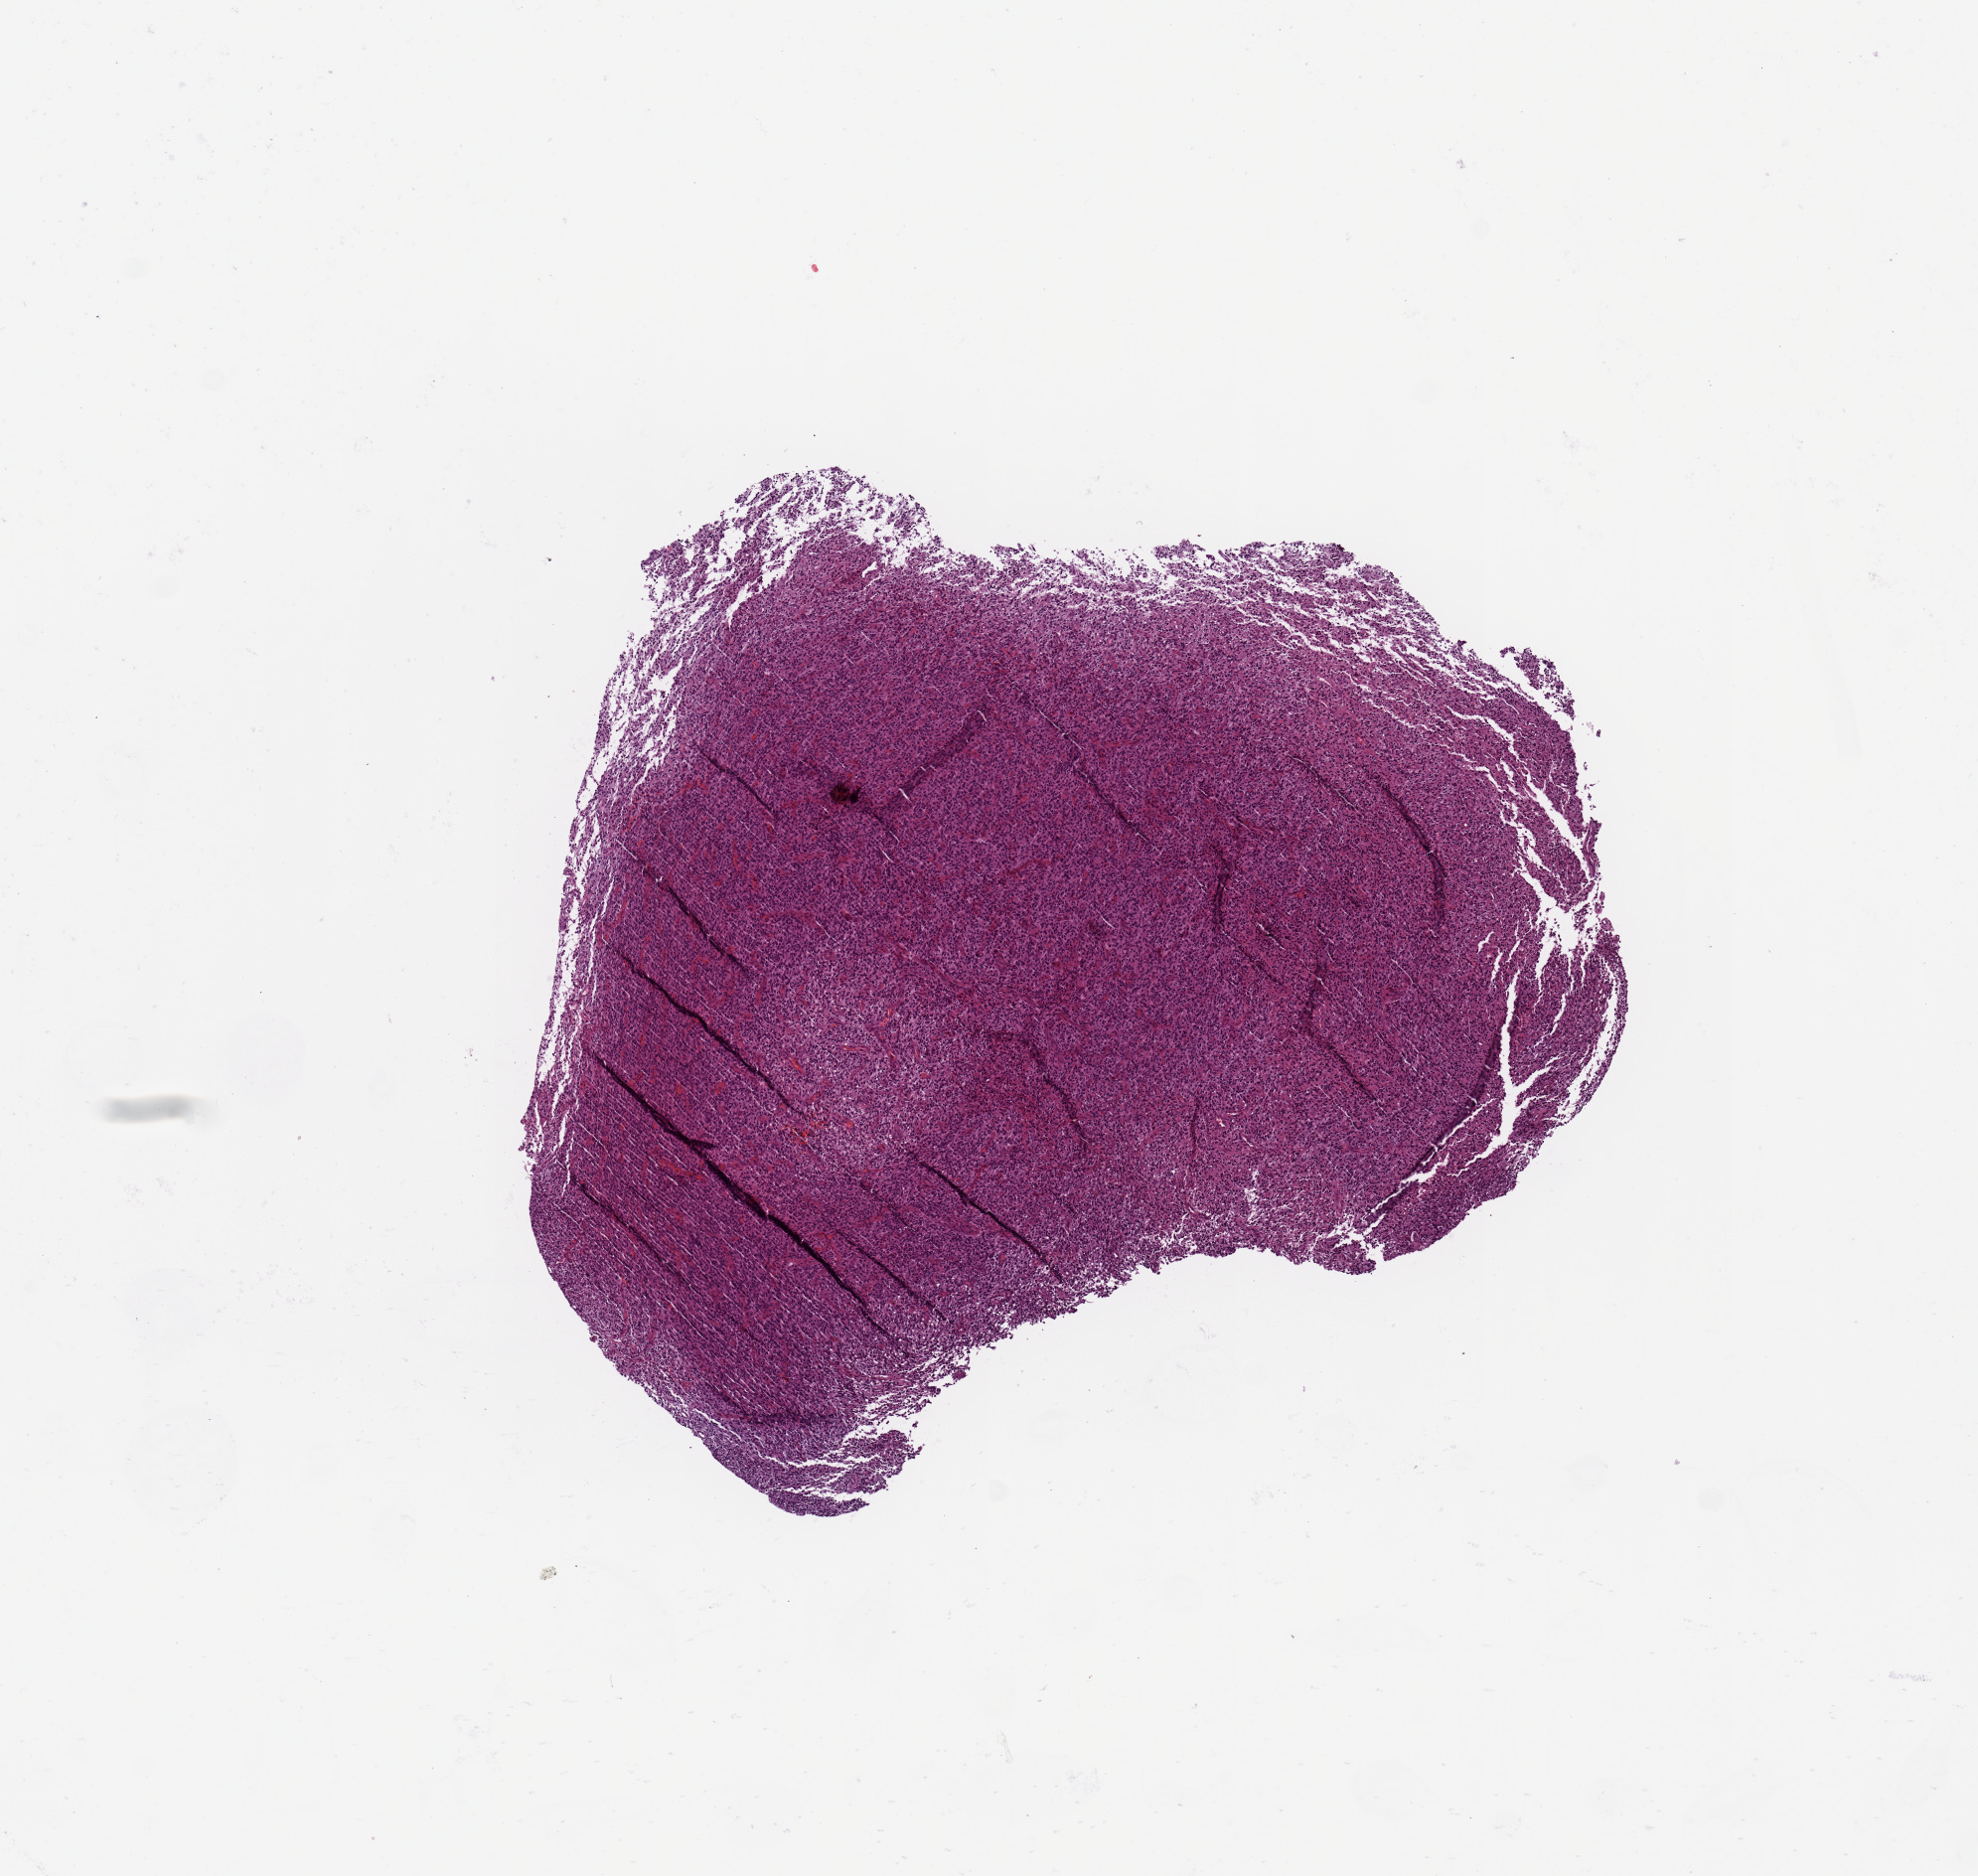
Digitized H&E-stained tissue section (whole slide), low-resolution overview of the scanned area, about 7.9 x 7.5 mm (acquisition: 20x scan), tumour tissue sample, sampled site: brain. Patient: male, age 54 years. Pathologist review of this section (percent, as recorded): tumour nuclei 90%, necrosis 0%.
- histologic diagnosis: Glioblastoma